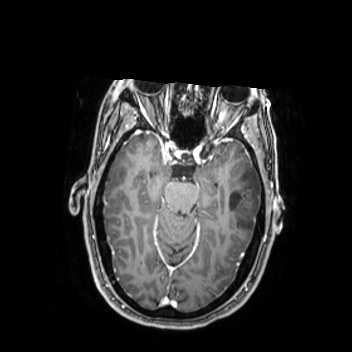
Brain MRI from a brain-tumour surgery series, one axial slice. Position 164 of 350 along the scan axis. T1-weighted post-contrast. 0.9 mm slice thickness. 352 × 352 image matrix, field of view 280 × 280 mm. From the clinical record (not read from this slice): histopathology: Oligodendroglioma; WHO grade: 2; IDH mutation: yes.
Structures marked on this image (manually delineated by an expert):
- tumour: bounding box (x1, y1, x2, y2) in pixels: (224, 163, 262, 236)